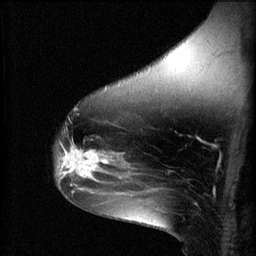
Breast MRI (dynamic contrast-enhanced), one sagittal slice. Position 42 of 60 along the scan axis. 3 images stored at this slice position (order not interpretable as contrast timing). 1.5 T. TE 4.2 ms, TR 8.2 ms. 2 mm slice thickness. 256 × 256 image matrix, field of view 180 × 180 mm. Female patient, age 49 years.
Structures marked on this image (semi-automatic segmentation, software-assisted and operator-edited):
- analysis volume of interest (the breast-tissue region the enhancement analysis was run in; not a lesion): bounding box [x1, y1, x2, y2] px = [56, 142, 109, 187]
- tumour enhancement mask (voxels above the 70 % enhancement threshold inside the analysis volume of interest): [57, 142, 109, 187]